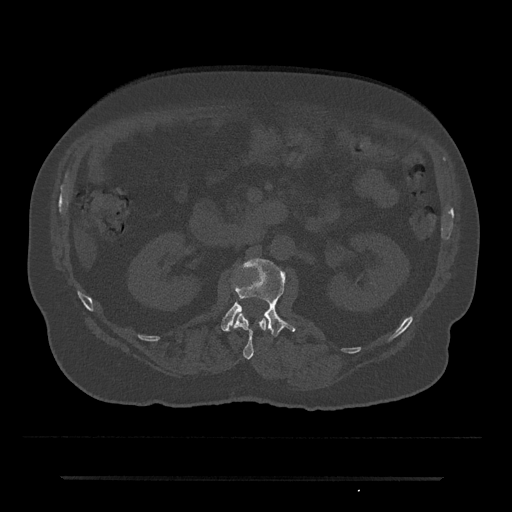
CT including the spine, one axial slice; slice 33 of 797 in the series (ordered by position); reconstruction kernel Br40s/3; 120 kVp; bone window (W 1800 / L 400 HU); 0.5 mm slice thickness; 512 × 512 image matrix, field of view 437 × 437 mm. Patient: male, 69 years. From the clinical record (not read from this slice): primary cancer: prostate.
Outlined on this slice (semi-automatically segmented with operator editing):
- L1 vertebra: bounding box [x1, y1, x2, y2] px = [233, 313, 266, 359]
- L2 vertebra: [221, 258, 295, 337]